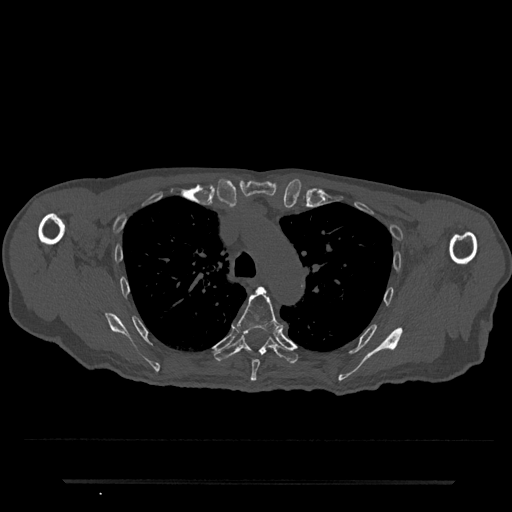
CT including the spine, one axial slice. Position 559 of 797 along the scan axis. Reconstruction kernel Br40s/3. 120 kVp. Bone window (W 1800 / L 400 HU). 0.5 mm slice thickness. 512 × 512 image matrix. Male patient, age 74 years. Case-level facts recorded for this patient, not image findings: primary cancer: prostate.
Structures marked on this image (semi-automatically segmented with operator editing):
- T5 vertebra: bounding box [x1, y1, x2, y2] px = [237, 287, 283, 382]
- T6 vertebra: [214, 333, 298, 364]